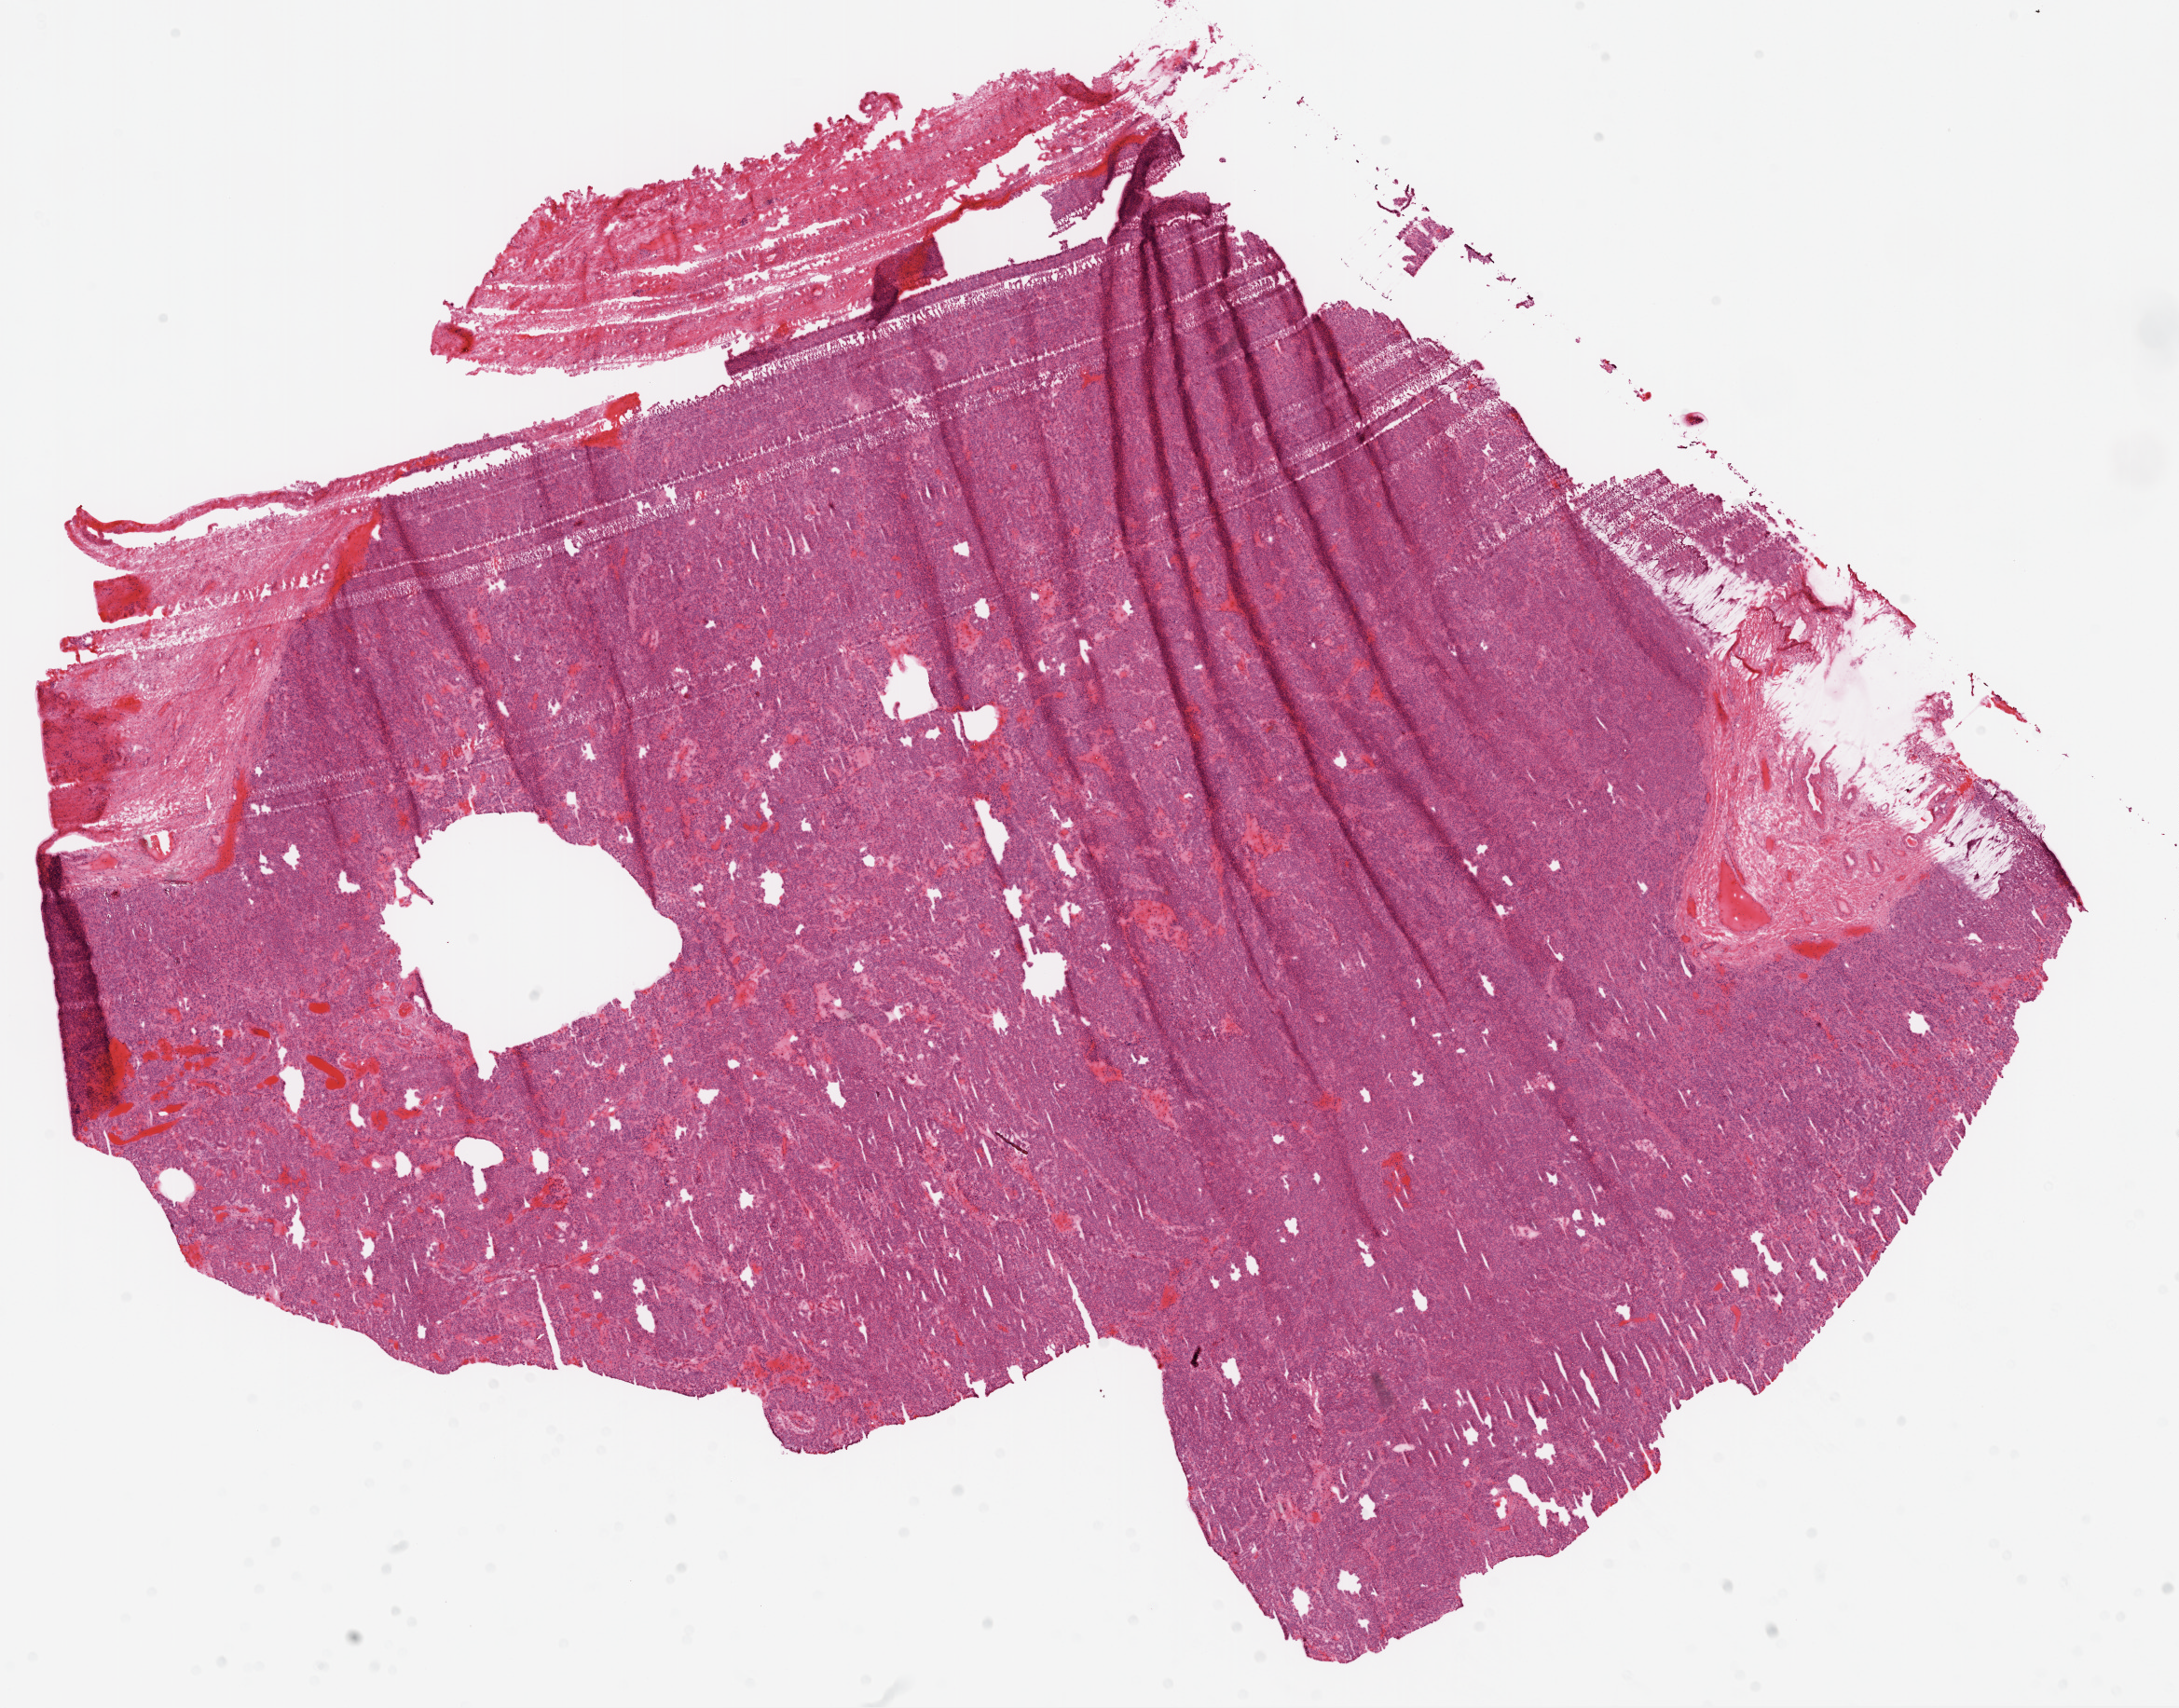
H&E-stained whole-slide image, low-resolution overview of the scanned area, about 18.9 x 14.8 mm. Frozen section. Primary tumour sample from the ovary. Patient: female, age at initial diagnosis 73 years. Histologic grade: G3 (poorly differentiated). Pathologist review of this section (percent, as recorded): tumour cells 90%, tumour nuclei 95%, normal cells 0%, stromal cells 5%, necrosis 5%.
* diagnosis: Serous cystadenocarcinoma, NOS
* FIGO stage: IIIC